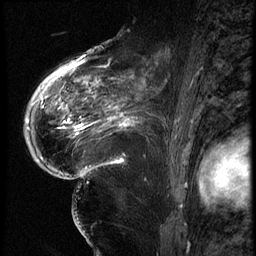
Breast MRI (dynamic contrast-enhanced), one sagittal slice; position 41 of 62 along the scan axis; 3 images stored at this slice position (order not interpretable as contrast timing); 1.5 T; TE 4.2 ms, TR 9 ms; 2.5 mm slice thickness; 256 × 256 image matrix. Female patient, age 56 years. Case-level facts recorded for this patient, not image findings: setting: breast cancer imaged before/during neoadjuvant chemotherapy; receptor status: HER2-positive.
Annotated regions visible in this slice (semi-automatically segmented with operator editing):
- analysis volume of interest (the breast-tissue region the enhancement analysis was run in; not a lesion): bounding box [x1, y1, x2, y2] px = [84, 75, 181, 153]
- tumour enhancement mask (voxels above the 140 % enhancement threshold inside the analysis volume of interest): [84, 75, 136, 131]